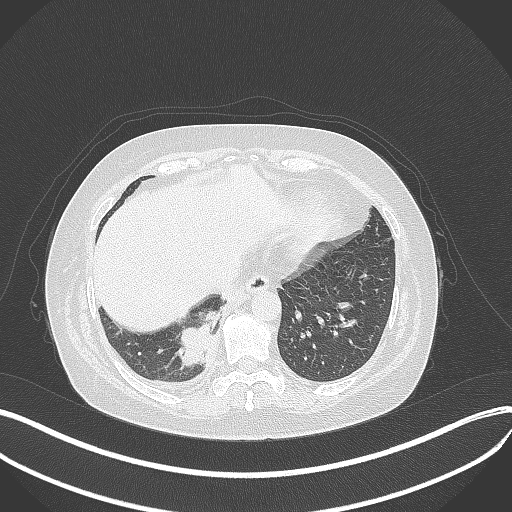
Chest CT, one axial slice; position 95 of 381 along the scan axis; 120 kVp; lung window (W 1500 / L -600 HU); 1 mm slice thickness; 512 × 512 image matrix, field of view 400 × 400 mm. Patient: female, 56 years. From the clinical record (not read from this slice): clinical TNM (as recorded): T2b N1 M0.
Outlined on this slice (rectangle marked by the reading radiologist):
- lung tumour (recorded histology: small cell carcinoma): bounding box <166,307,219,375> (left, top, right, bottom; pixels)